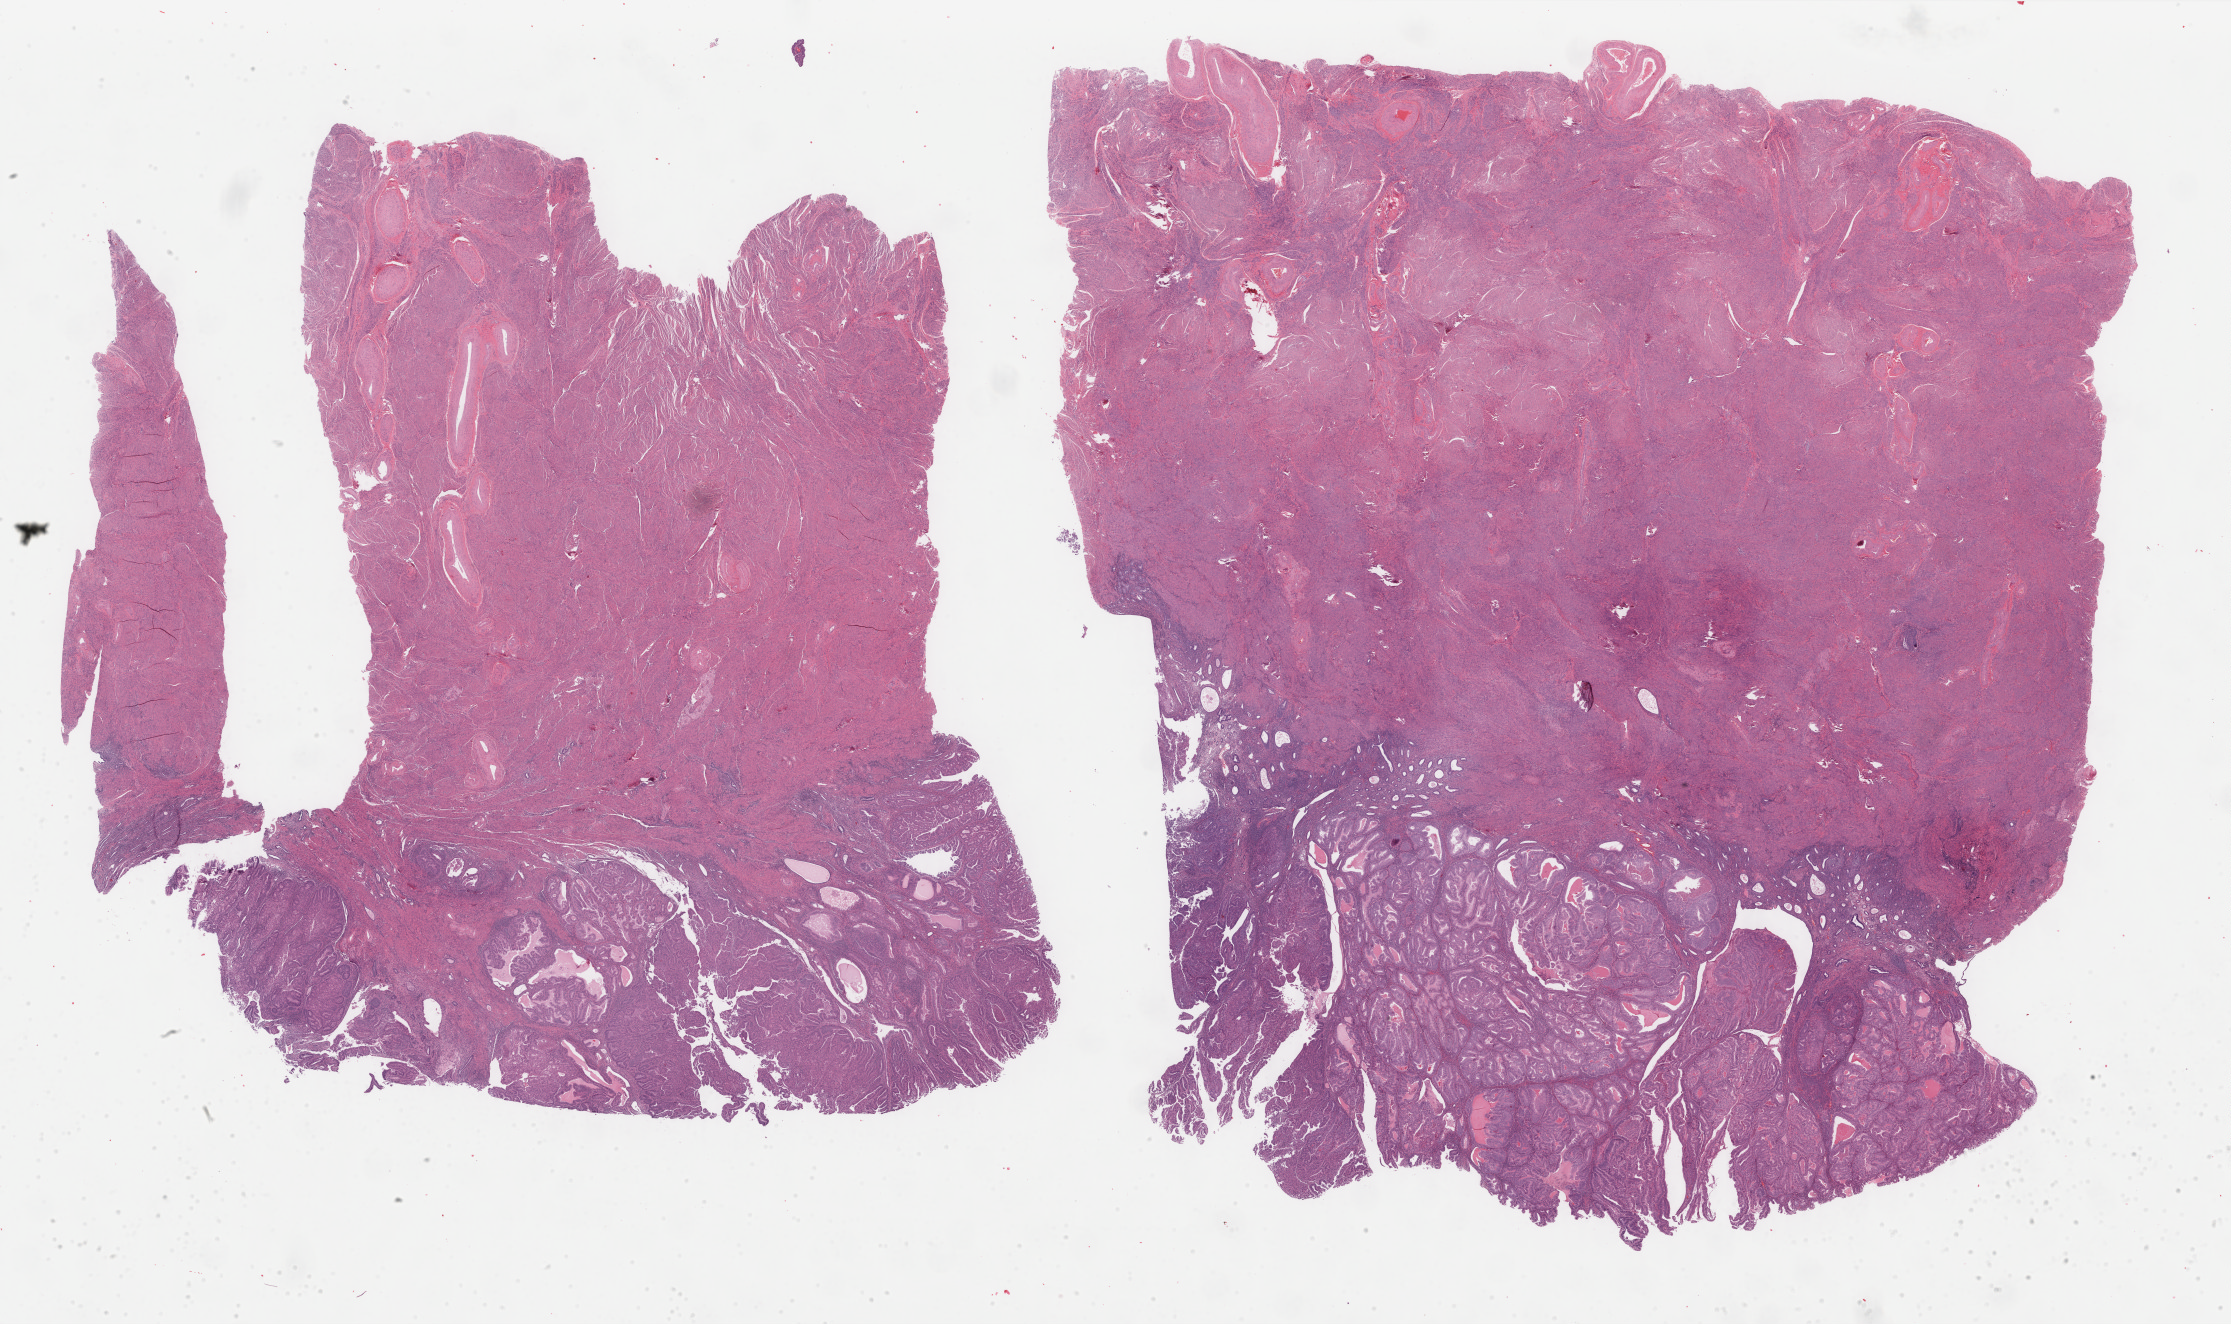
H&E-stained whole-slide image, whole scanned area (about 35.4 x 21.0 mm, acquisition: 40x scan) shown as a low-resolution overview; FFPE section; uterus, primary tumour sample. Female patient; age at initial diagnosis 54 years. Histologic grade: G2 (moderately differentiated).
Histologic diagnosis: Endometrioid adenocarcinoma, NOS (endometrium). FIGO stage: IB.